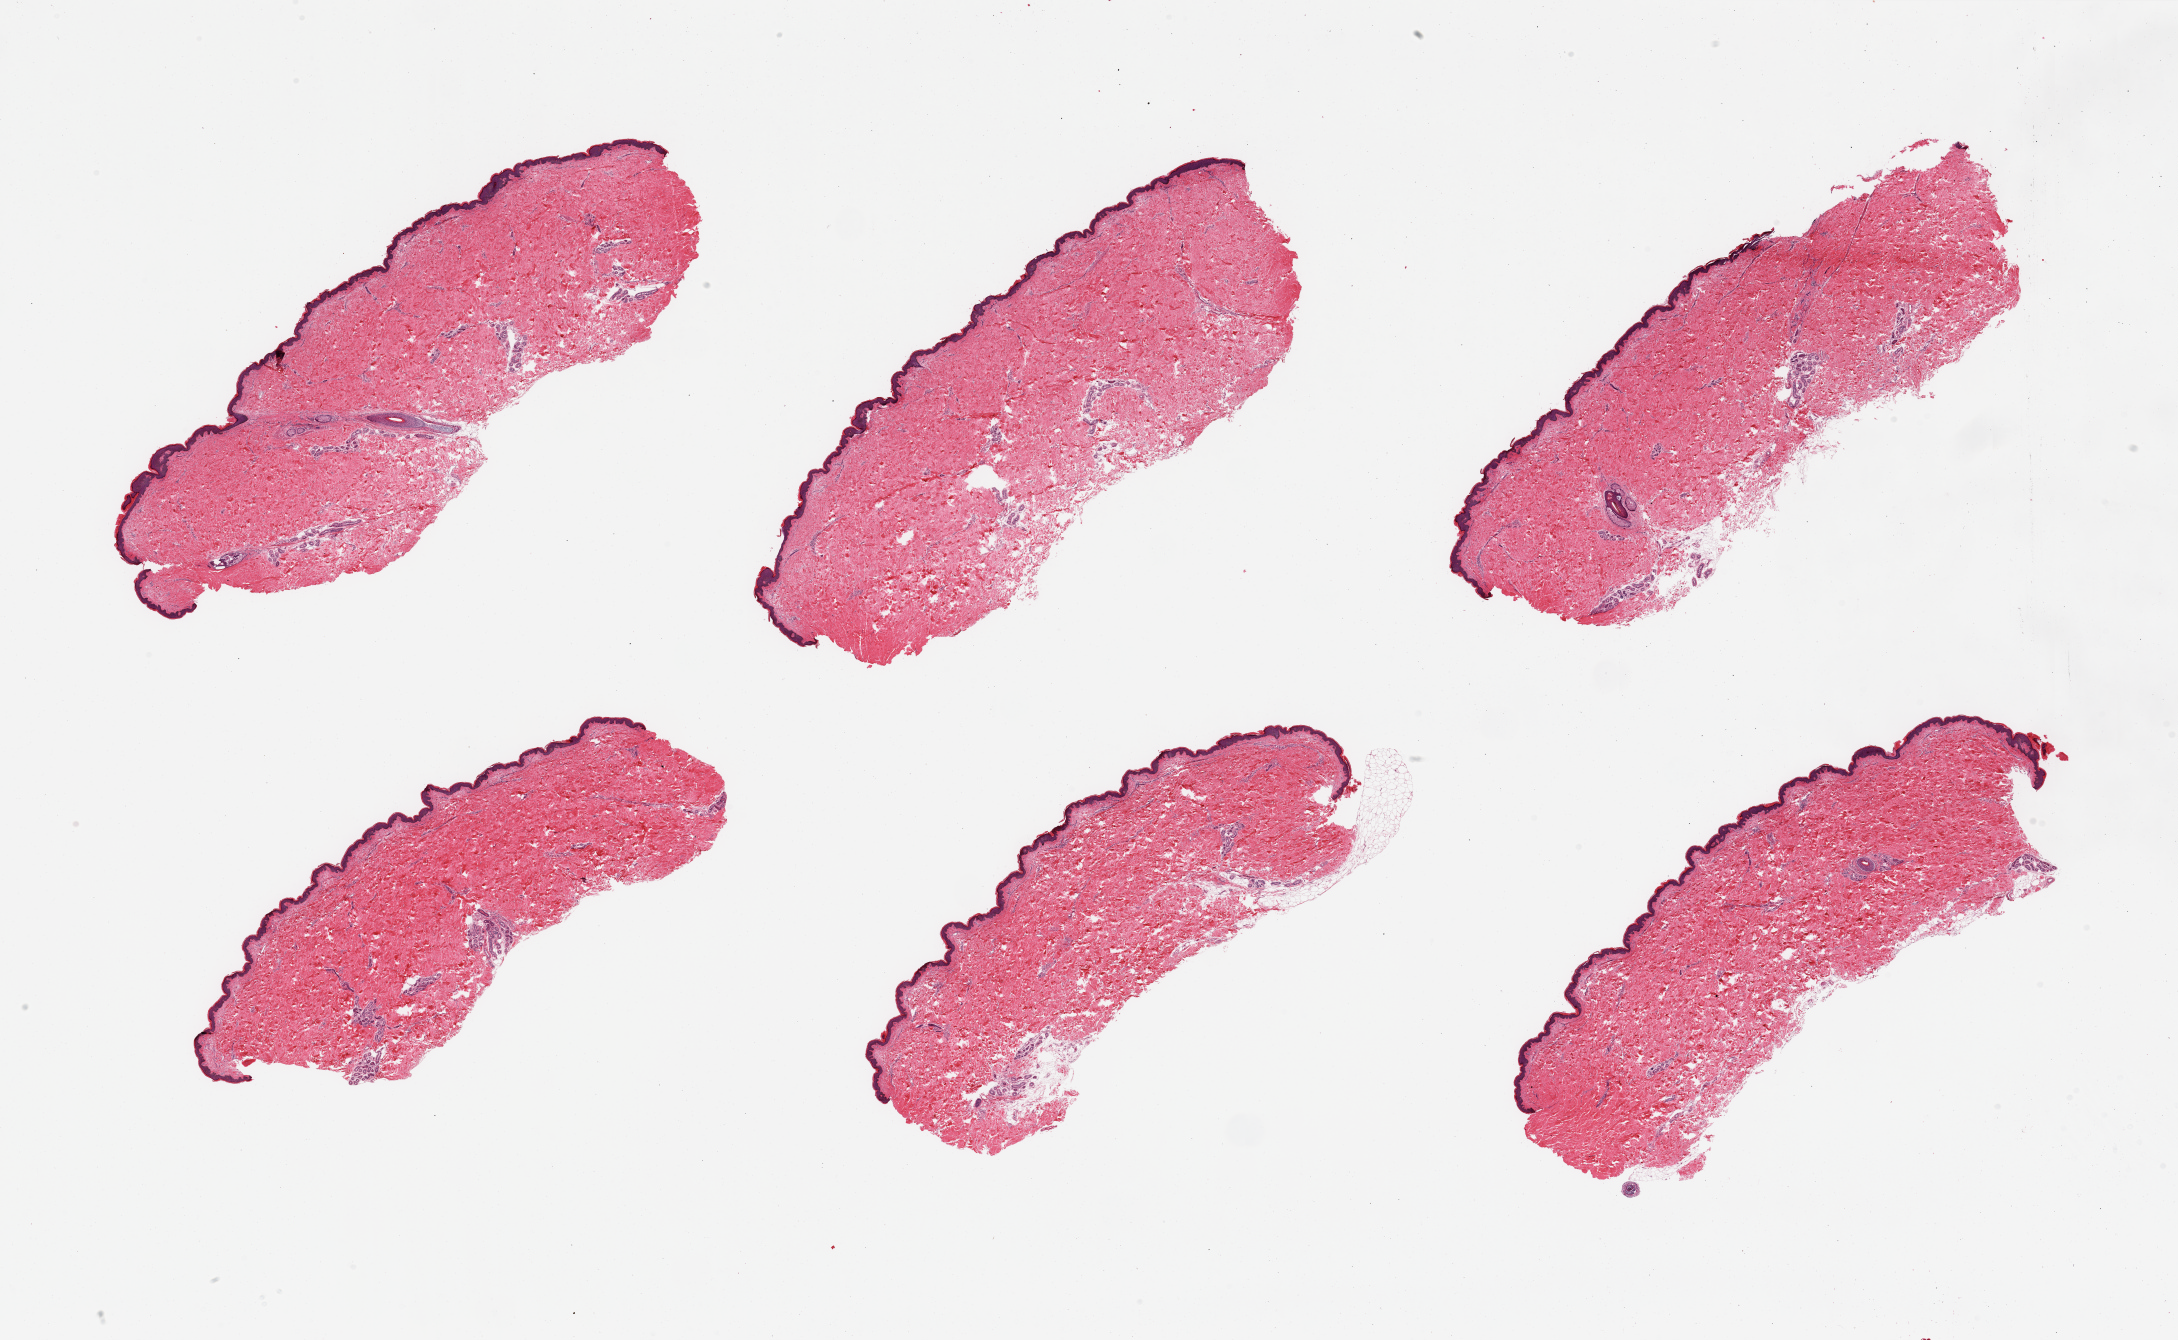
Whole-slide image, haematoxylin and eosin stain, low-resolution overview of the scanned area, about 34.5 x 21.2 mm. PAXgene-fixed, paraffin-embedded tissue. Sampled site (target tissue): skin of suprapubic region. Donor tissue sample.
- reviewer comment on this tissue sample: 6 pieces; well trimmed; <5% dermal fat